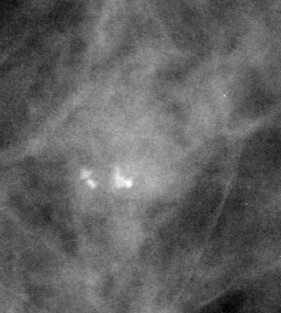
Crop from a digitized film mammogram around one marked abnormality; left breast; CC view.
Calcifications, morphology punctate, distribution clustered; BI-RADS assessment category 3; pathology result (as recorded, not read from the image): benign.